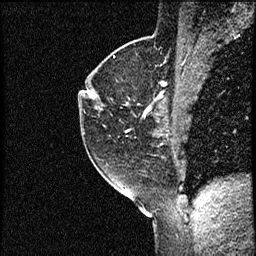
Breast MRI (dynamic contrast-enhanced), one sagittal slice; dynamic contrast-enhanced study with each time point stored as its own series, time point 2 of 3 at this slice position (early post-contrast, ordered by acquisition time); 1.5 T; TE 4.2 ms, TR 17.3 ms; 2 mm slice thickness; 256 × 256 image matrix, field of view 200 × 200 mm. Female patient. From the clinical record (not read from this slice): setting: breast cancer imaged before/during neoadjuvant chemotherapy; receptor status: HER2-positive.
Outlined on this slice (semi-automatic segmentation, software-assisted and operator-edited):
- analysis volume of interest (the breast-tissue region the enhancement analysis was run in; not a lesion): box from (x=78, y=50) to (x=156, y=155) px
- tumour enhancement mask (voxels above the 100 % enhancement threshold inside the analysis volume of interest): (x=87, y=90)–(x=97, y=98)